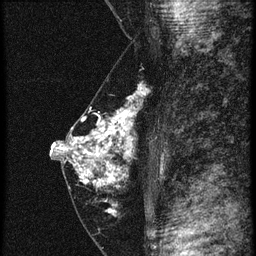
Breast MRI (dynamic contrast-enhanced), one sagittal slice; slice 28 of 60 in the series (ordered by position); 4 images stored at this slice position (order not interpretable as contrast timing); 1.5 T; TE 4.2 ms, TR 20.4 ms; 1.5 mm slice thickness; 256 × 256 image matrix, field of view 180 × 180 mm. Patient: female, 46 years. Case-level facts recorded for this patient, not image findings: setting: breast cancer imaged before/during neoadjuvant chemotherapy; receptor status: triple-negative.
Structures marked on this image (semi-automatic segmentation, software-assisted and operator-edited):
- analysis volume of interest (the breast-tissue region the enhancement analysis was run in; not a lesion): box from (x=67, y=88) to (x=149, y=201) px
- tumour enhancement mask (voxels above the 90 % enhancement threshold inside the analysis volume of interest): (x=67, y=94)–(x=141, y=187)